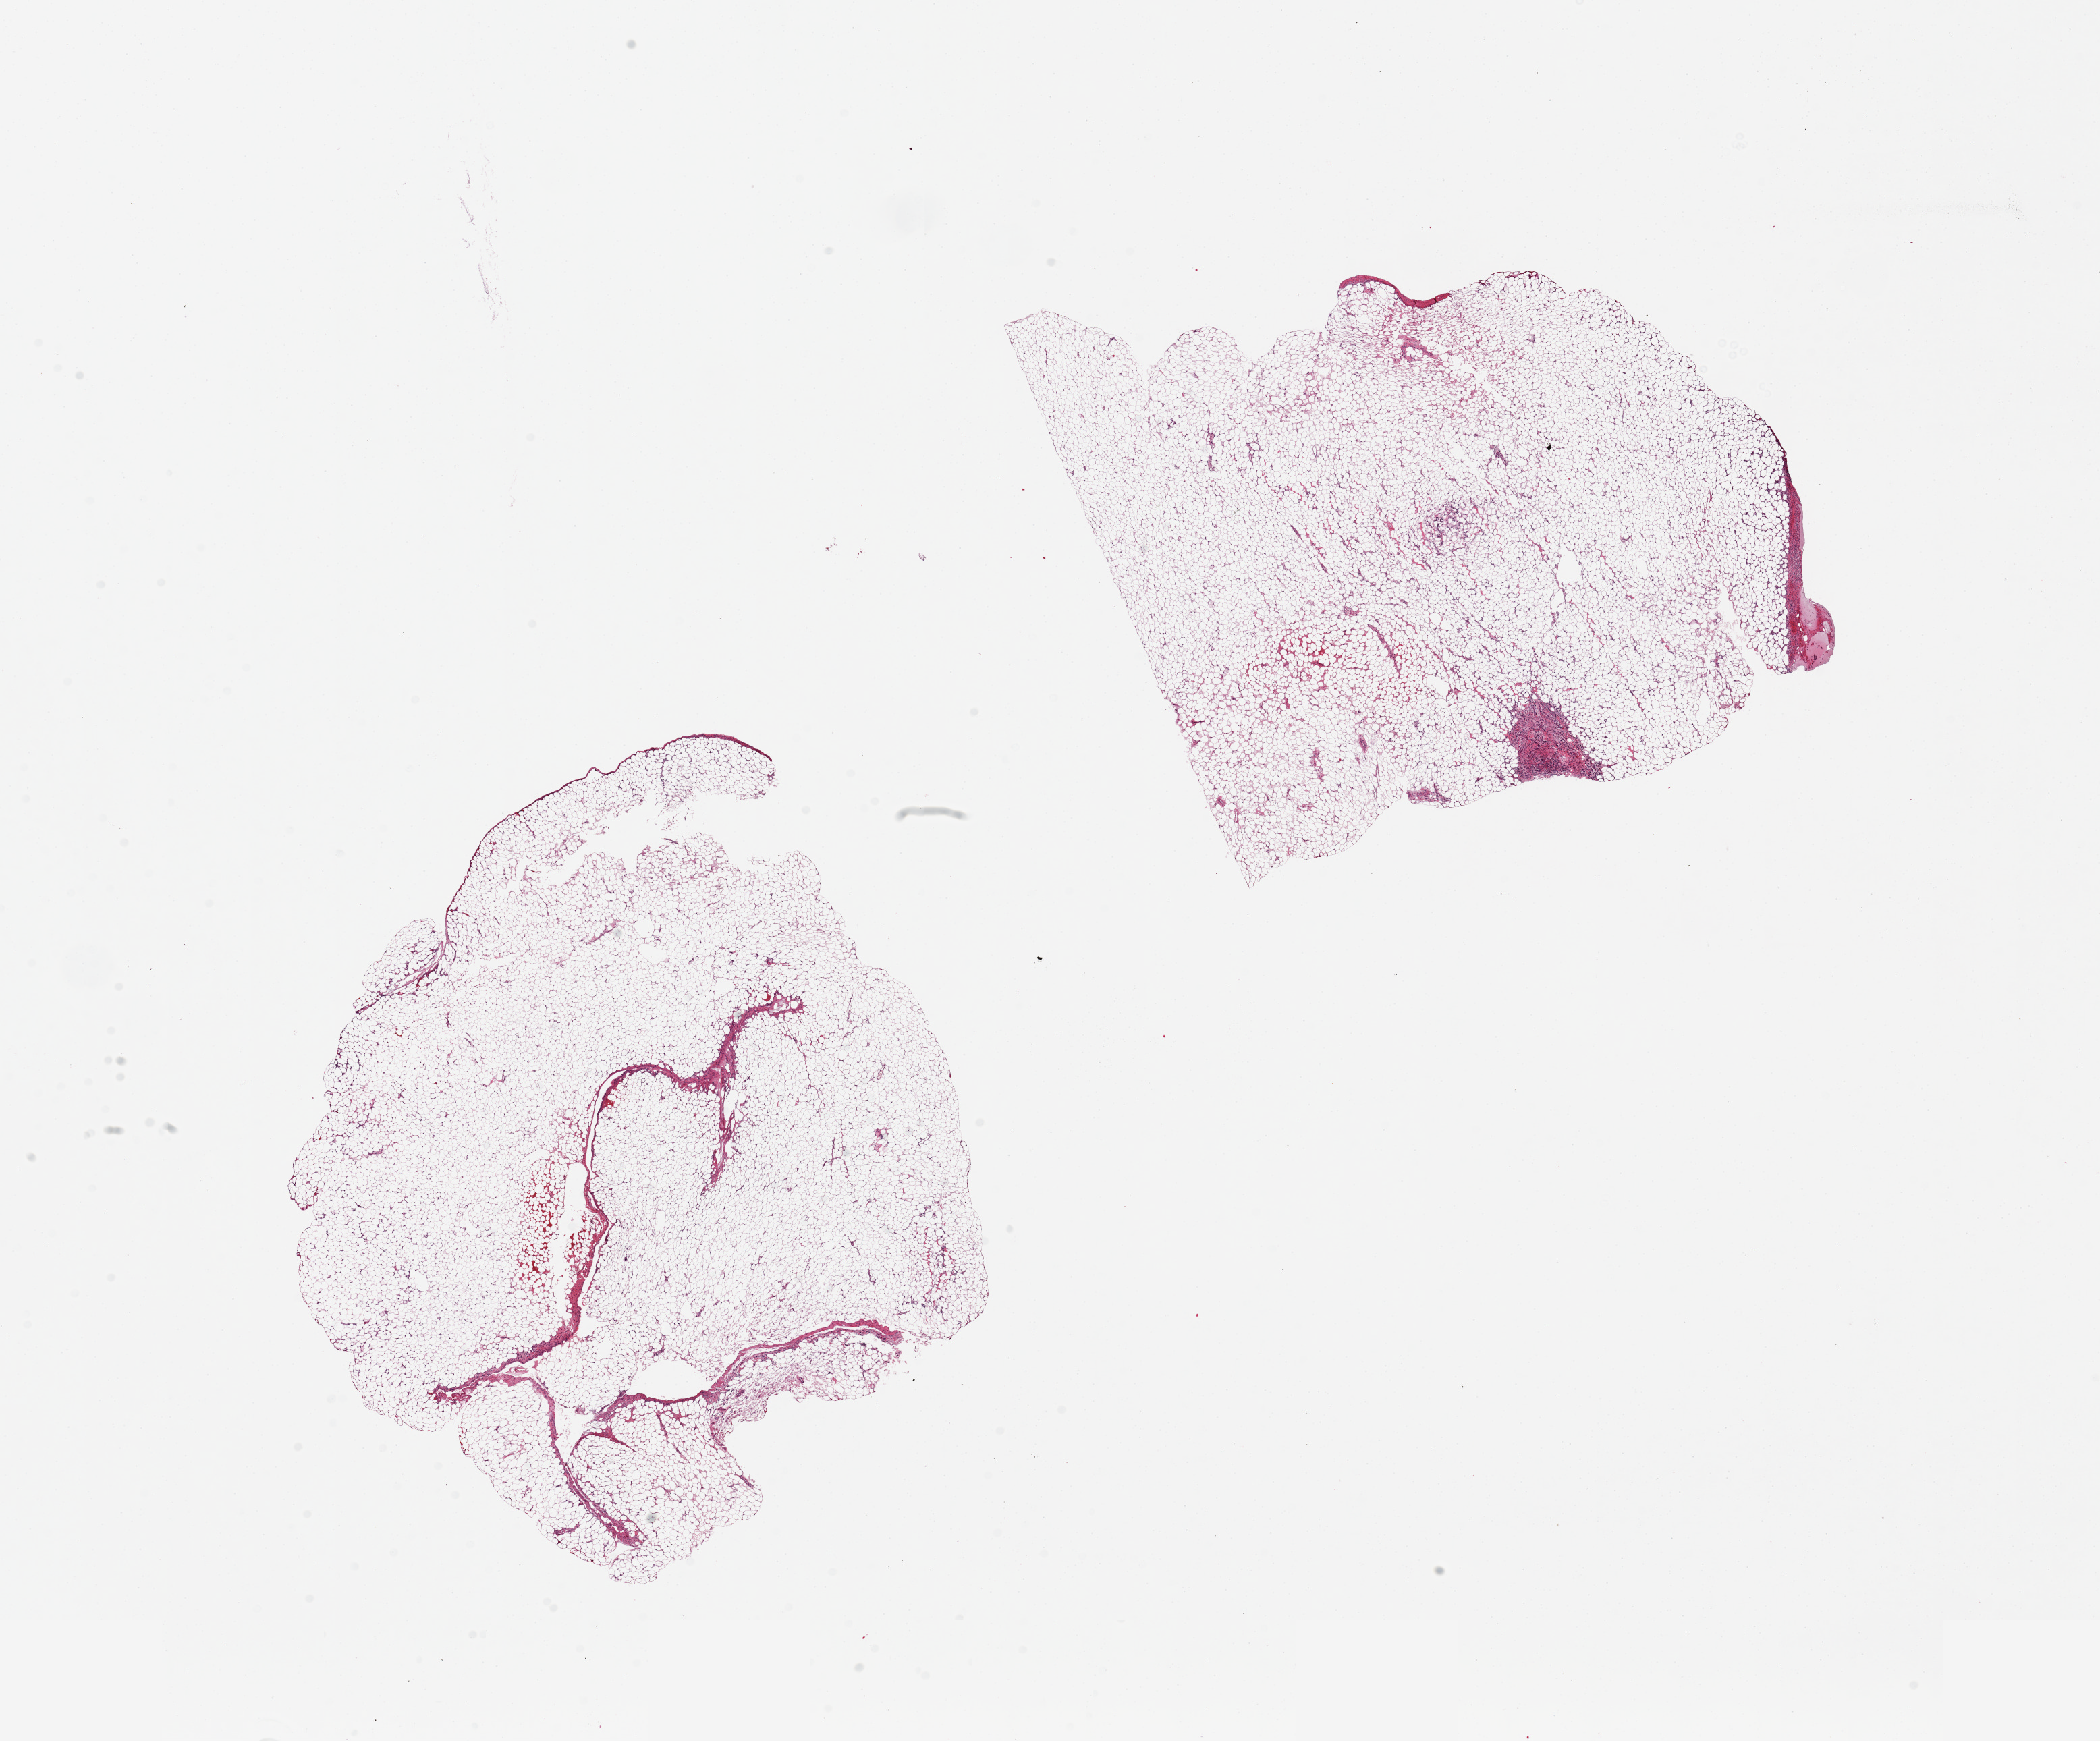
Whole-slide image, haematoxylin and eosin stain — shown as a low-resolution overview of the whole scanned area (about 24.6 x 20.4 mm); PAXgene-fixed, paraffin-embedded tissue; sampled site (target tissue): auricular appendage; donor tissue sample. Male donor.
* reviewer comment on this tissue sample: 2 pieces, 8x8 & 8x7.5mm; entirely adipose tissue, no muscle